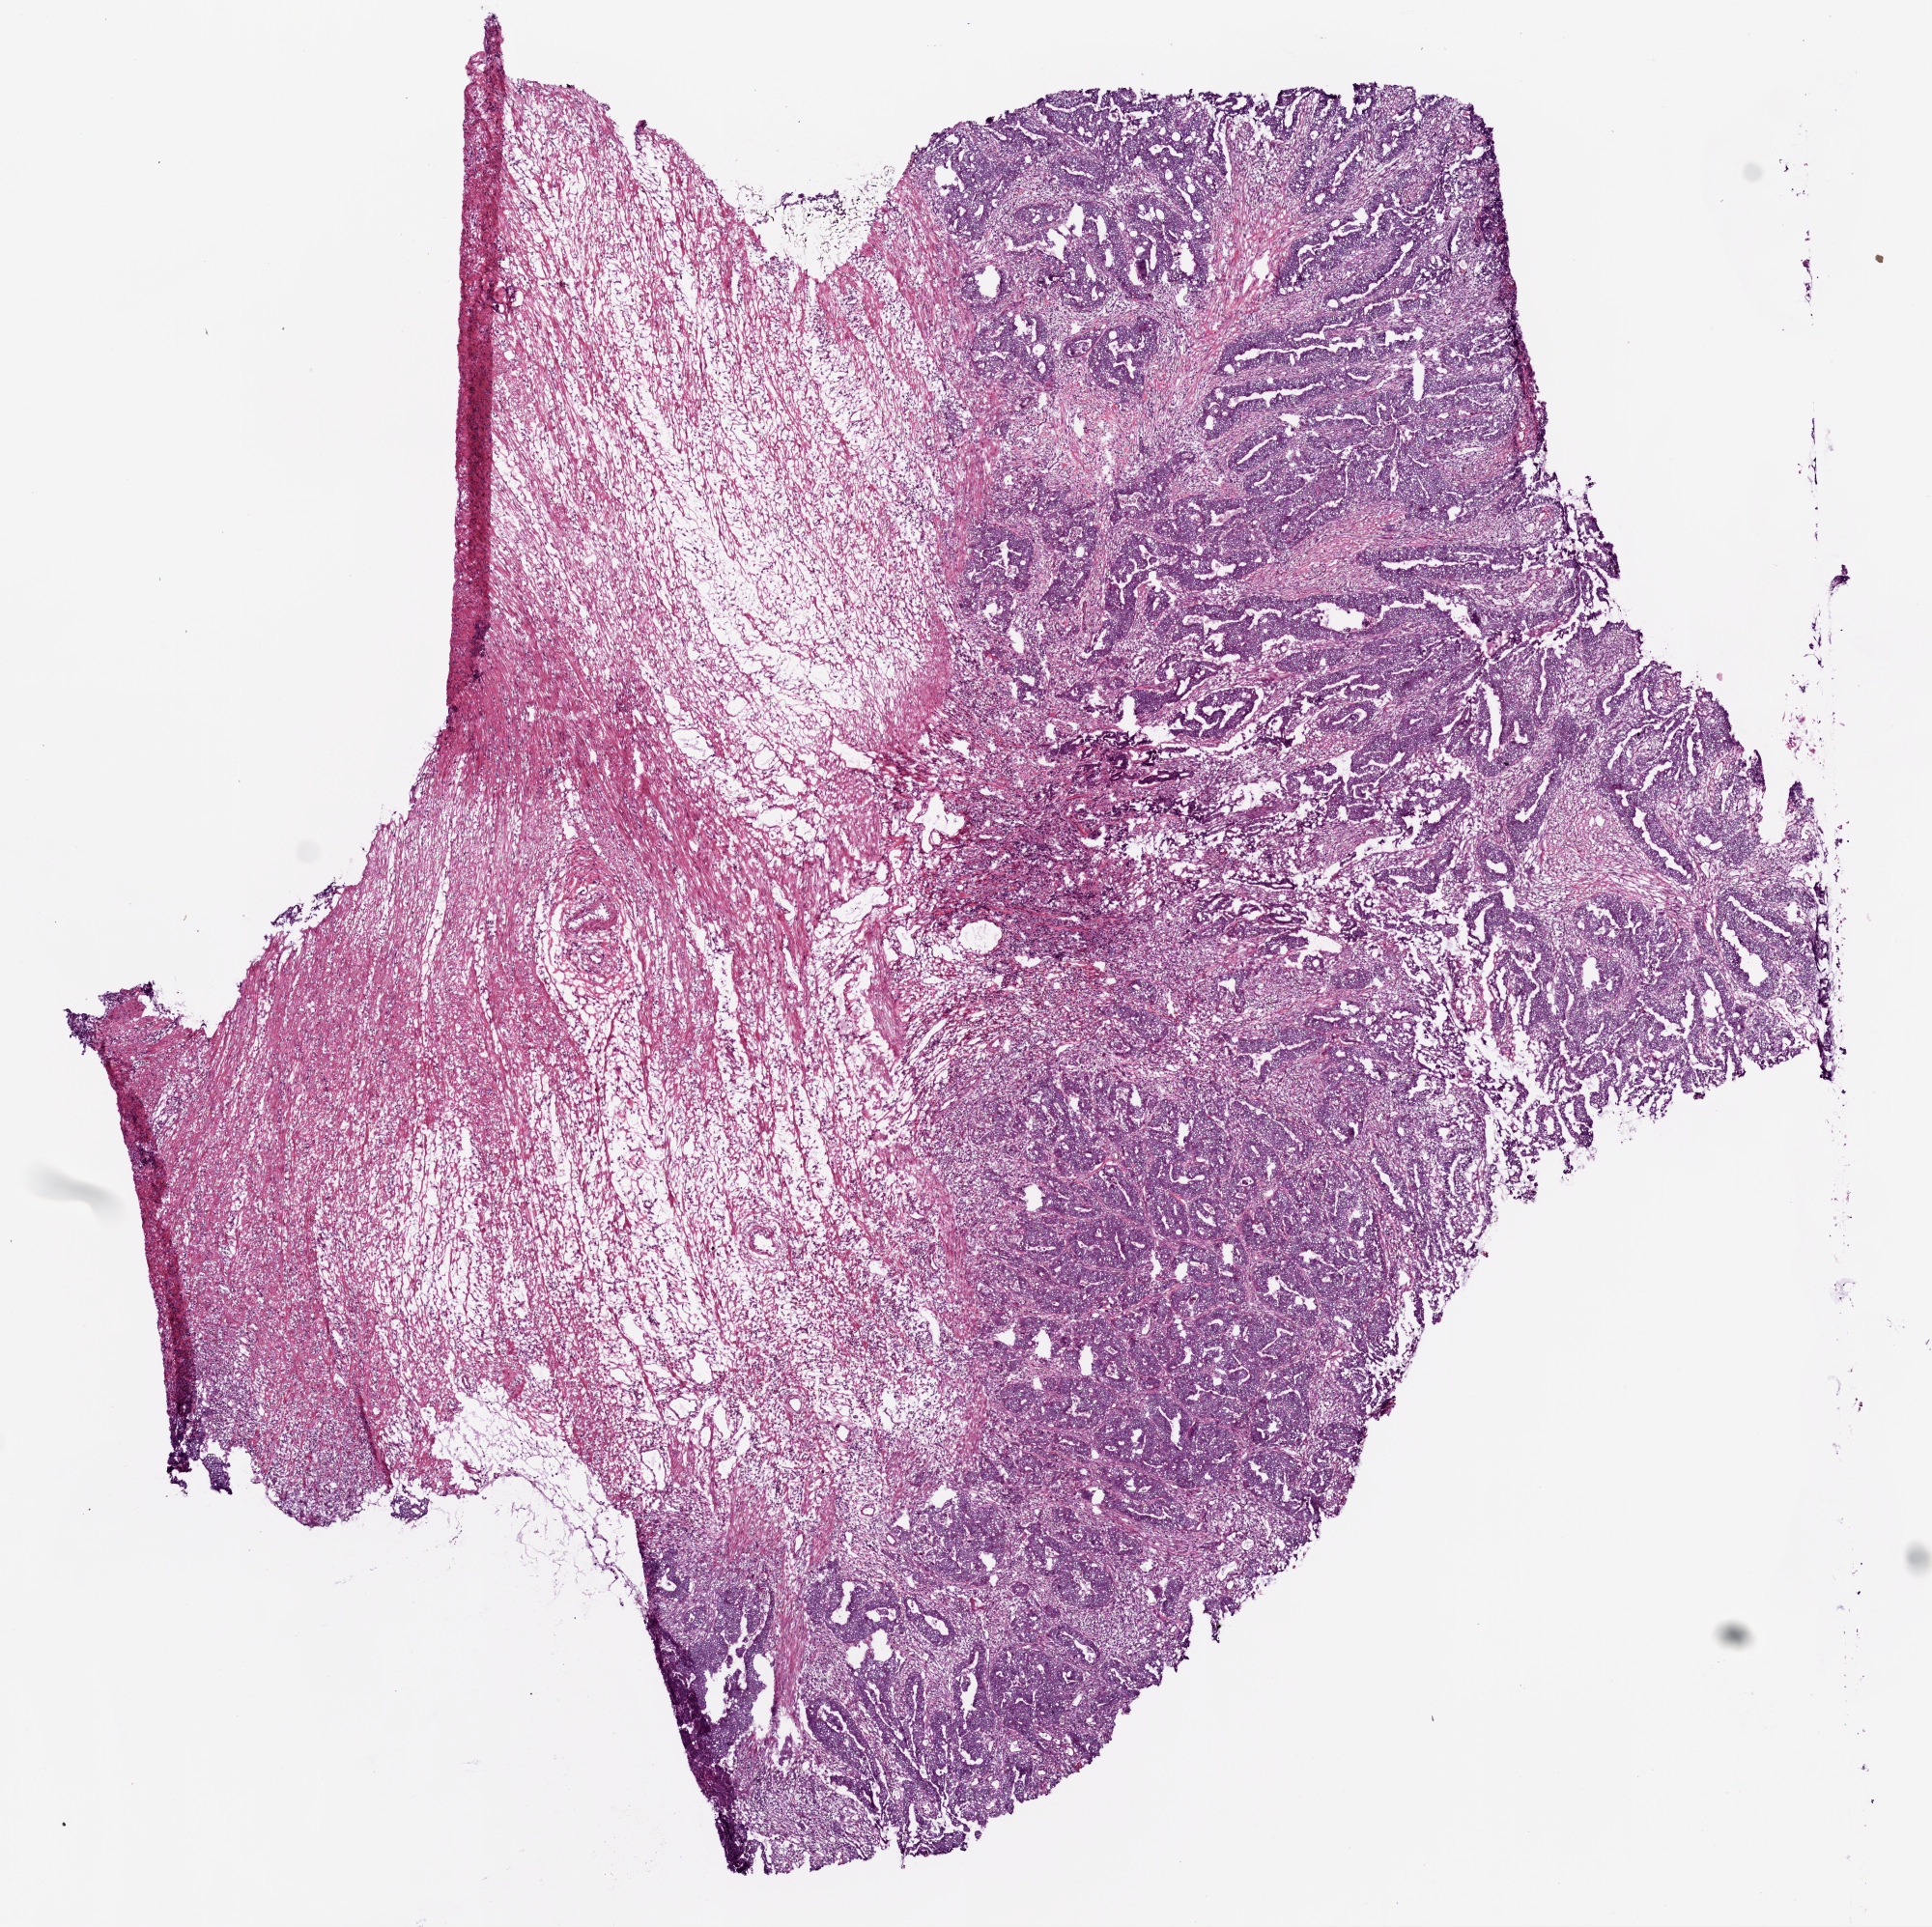
Digitized H&E tissue section (whole slide) — a low-resolution overview of the entire scanned area, about 8.0 x 8.0 mm (slide scanned at 20x); frozen section from the top of the tissue portion; sample: primary tumour, colon. Male, age 65 years at initial diagnosis. Slide review estimates, as recorded: tumour cells 60%, tumour nuclei 70%, normal cells 40%, stromal cells 0%, necrosis 0%. Infiltration values recorded for this section: lymphocyte infiltration 10%, monocyte infiltration 1%, neutrophil infiltration 2%.
Lymph nodes positive (case pathology): 1 of 42 examined. AJCC pathologic stage: IIIB. Diagnosis: Adenocarcinoma, NOS.